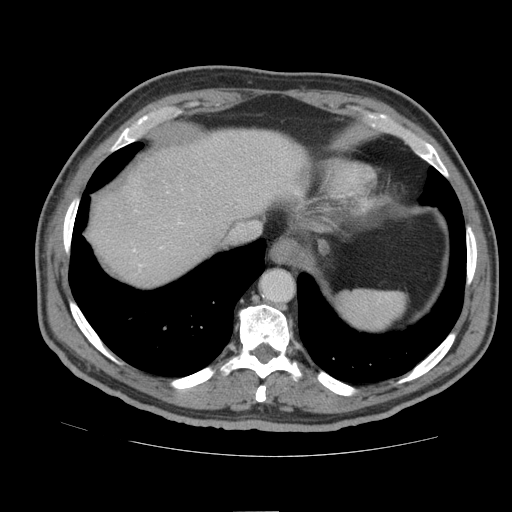
Contrast-enhanced abdominal CT (liver protocol), one axial slice; slice 75 of 105 in the series (ordered by position); 140 kVp; soft-tissue window (W 400 / L 40 HU); 2.5 mm slice thickness; 512 × 512 image matrix, field of view 380 × 380 mm. Case-level facts recorded for this patient, not image findings: diagnosis: hepatocellular carcinoma (patient treated with transarterial chemoembolisation; whether this scan precedes or follows treatment is not stated here); TNM stage (as recorded): Stage-IIIB; Child-Pugh class: A; tumour nodularity: multinodular.
Structures marked on this image (semi-automatically segmented with operator editing):
- abdominal aorta: bounding box (x1, y1, x2, y2) in pixels: (262, 271, 293, 301)
- liver parenchyma outside the tumour (the mass and vessels are separate outlines, so this box may not span the whole liver): (90, 130, 308, 286)